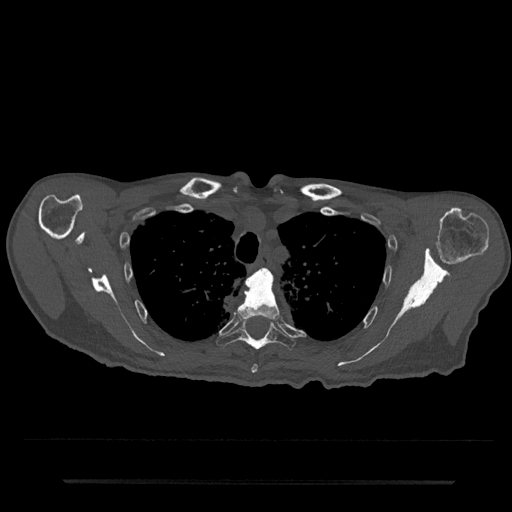
CT including the spine, one axial slice; slice 600 of 797 in the series (ordered by position); reconstruction kernel Br40s/3; 120 kVp; bone window (W 1800 / L 400 HU); 0.5 mm slice thickness; 512 × 512 image matrix. Patient: male, 74 years. Case-level facts recorded for this patient, not image findings: primary cancer: prostate.
Structures marked on this image (semi-automatic segmentation, software-assisted and operator-edited):
- T3 vertebra: bounding box [x1, y1, x2, y2] px = [264, 269, 270, 275]
- T4 vertebra: [237, 269, 280, 373]
- T5 vertebra: [216, 317, 296, 350]